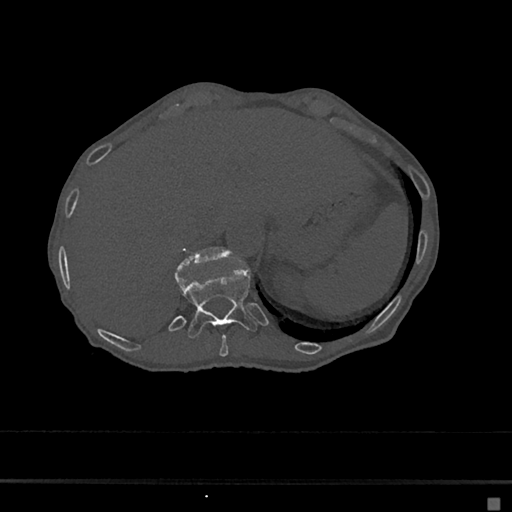
CT including the spine, one axial slice; slice 177 of 797 in the series (ordered by position); reconstruction kernel Br40s/3; 120 kVp; bone window (W 1800 / L 400 HU); 512 × 512 image matrix. Patient: female, 68 years. Case-level facts recorded for this patient, not image findings: primary cancer: renal.
Annotated regions visible in this slice (semi-automatic segmentation, software-assisted and operator-edited):
- T10 vertebra: bounding box [x1, y1, x2, y2] px = [219, 335, 228, 357]
- T11 vertebra: [175, 267, 257, 339]
- T12 vertebra: [176, 247, 232, 273]